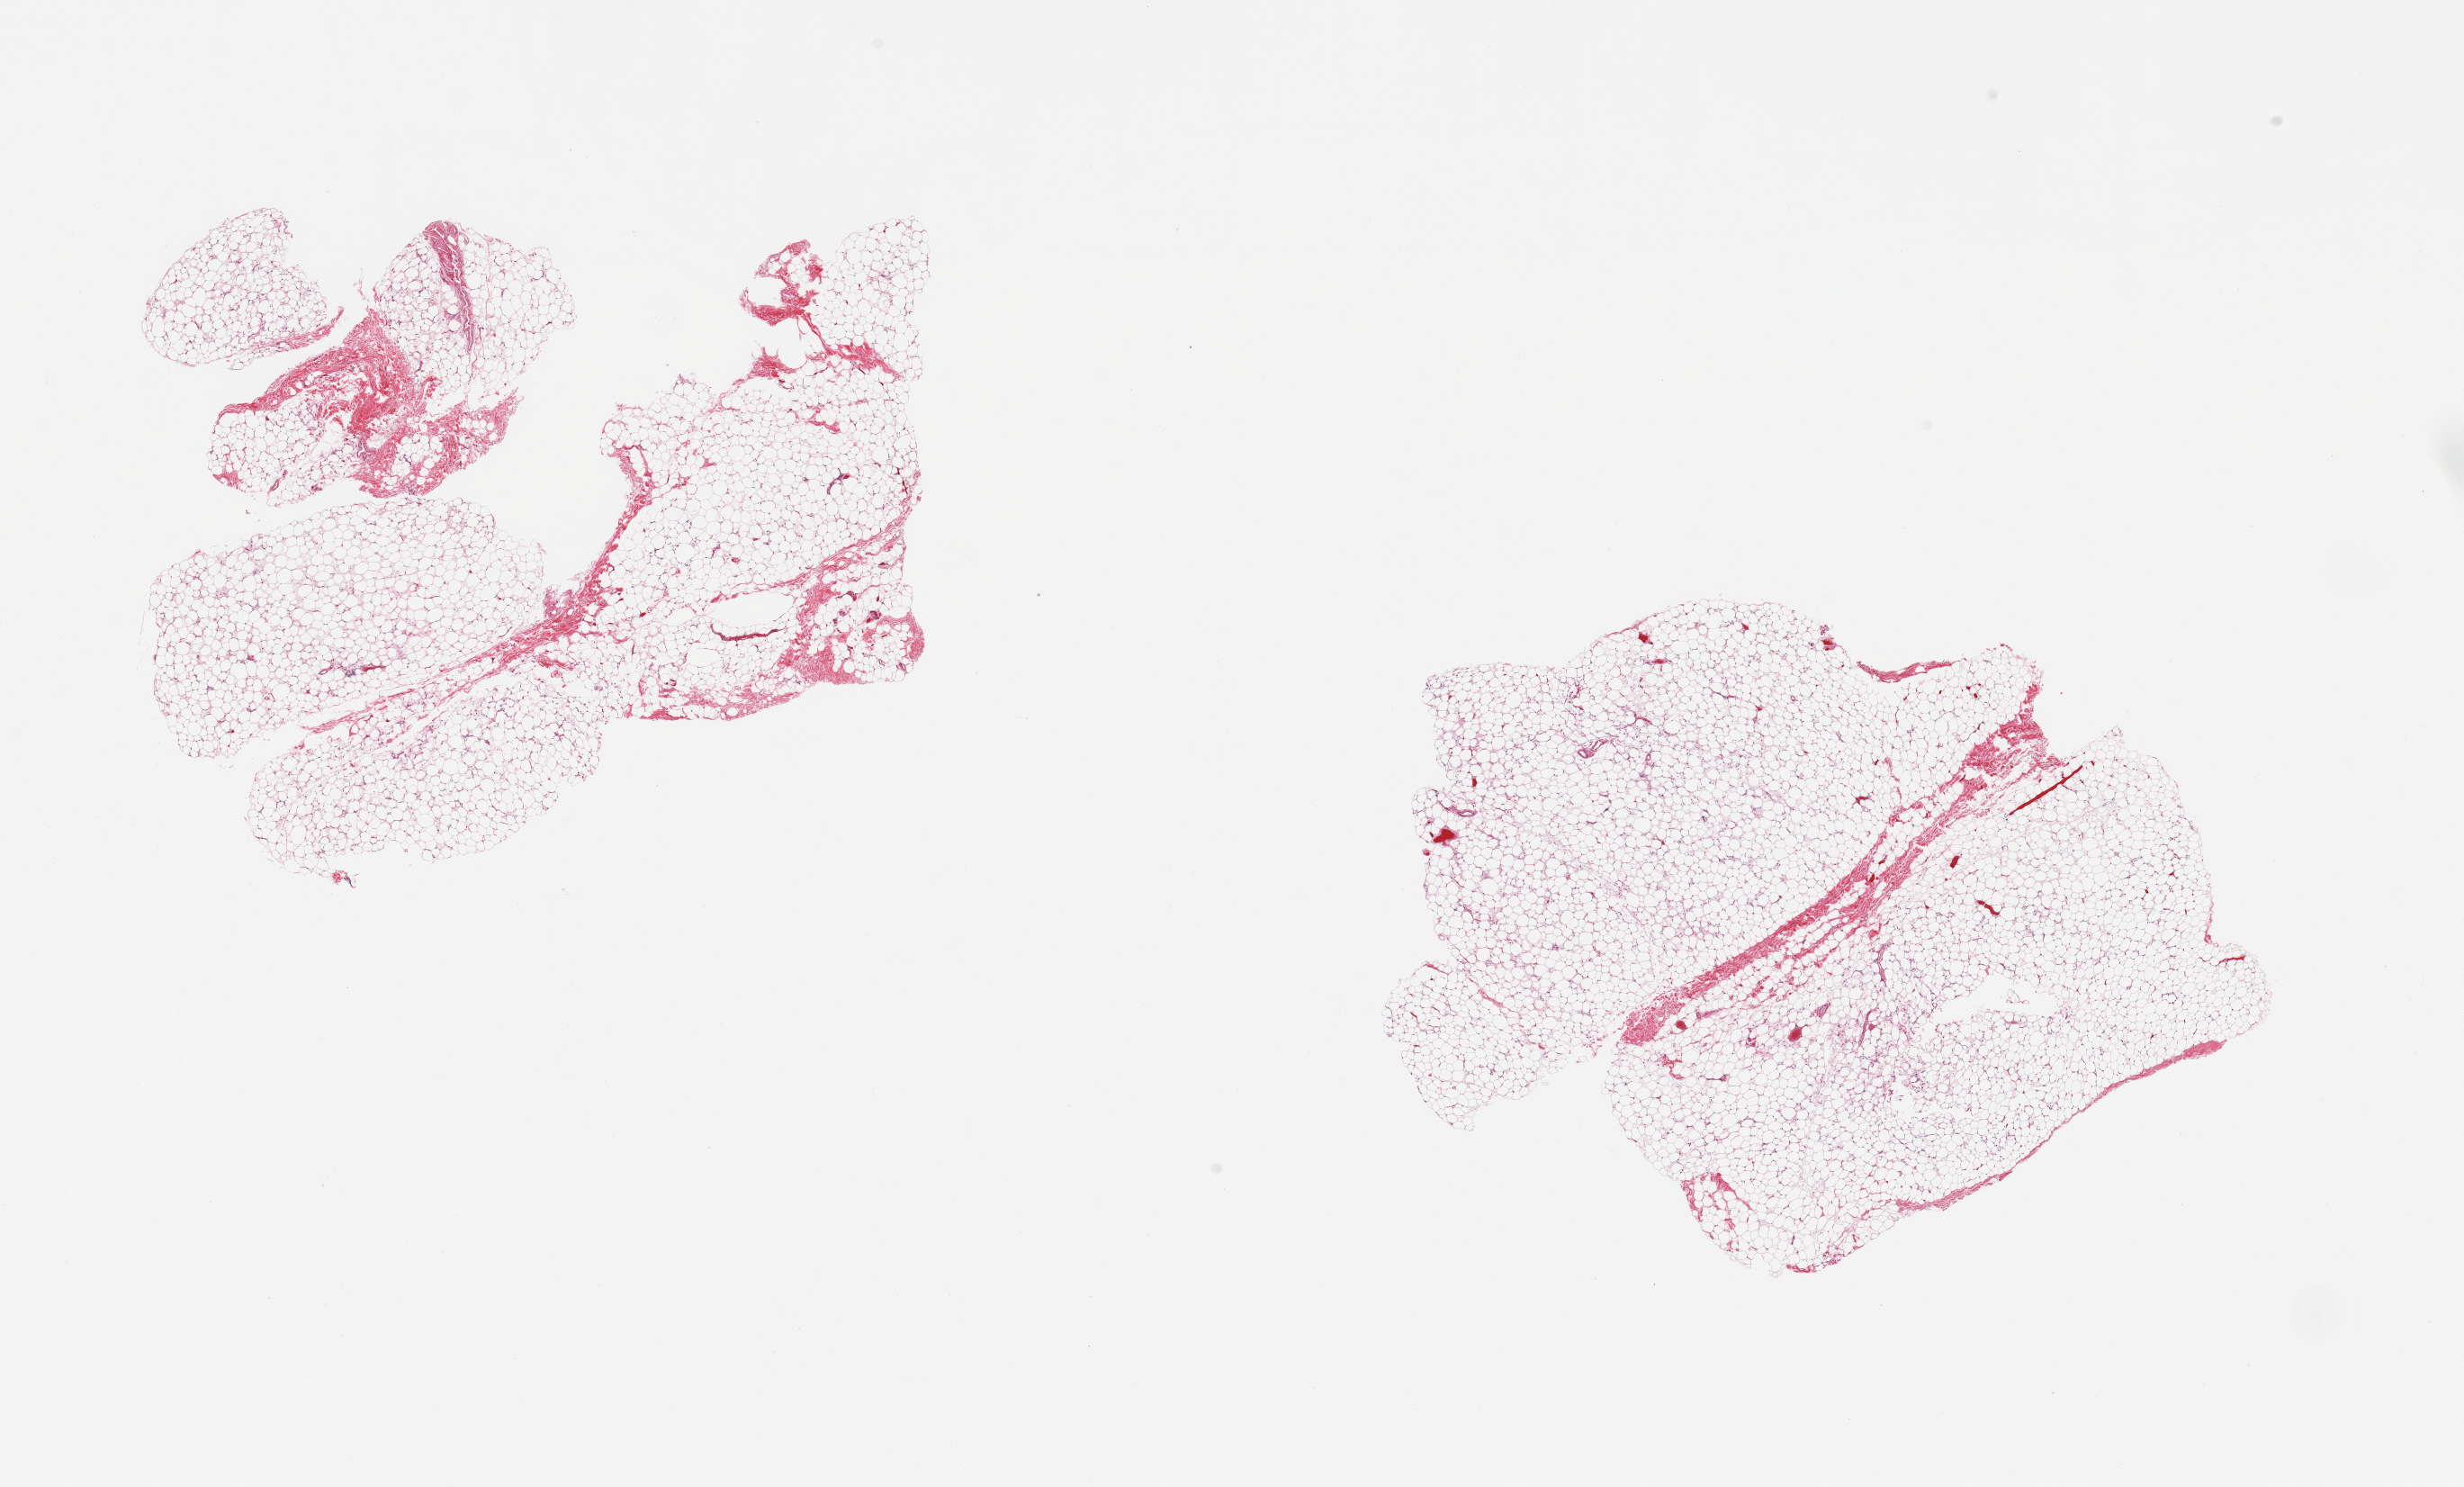
Whole-slide image, H&E stain, shown as a low-resolution overview of the whole scanned area (about 21.7 x 13.1 mm); PAXgene-fixed paraffin-embedded (PFPE) section; section of breast (target tissue); donor tissue sample. Male donor.
Pathologist's review note for this sample: 2 pieces; predominantly fat, up to 10% fibrocollagenous stroma, no ductal elements.